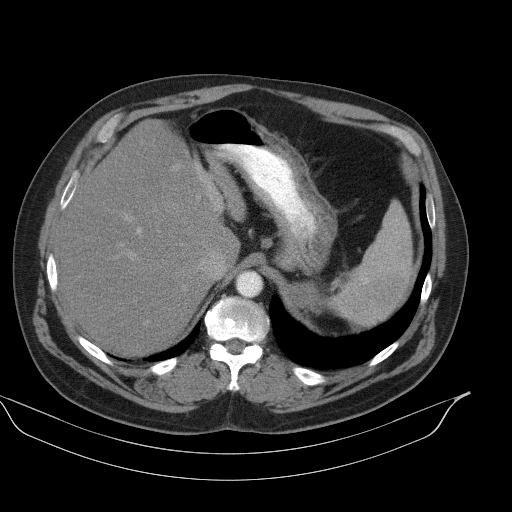
Contrast-enhanced abdominal CT, one axial slice; position 76 of 92 along the scan axis; reconstruction kernel B41s; 130 kVp; soft-tissue window (W 400 / L 40 HU); 512 × 512 image matrix, field of view 449 × 449 mm. Male patient, age 56 years. Case-level facts recorded for this patient, not image findings: diagnosis: adrenocortical carcinoma; tumour side: left adrenal; tumour size at pathology: 15 cm; Ki-67 index: 35 %; stage (as recorded): 4.
Annotated regions visible in this slice (semi-automatically segmented with operator editing):
- mass: box from (x=292, y=283) to (x=322, y=308) px